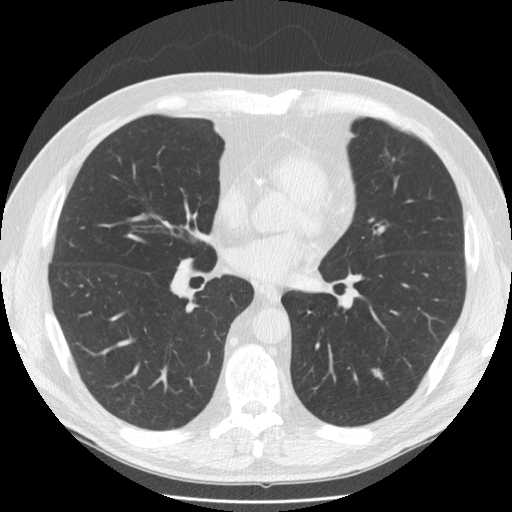
Axial slice from a low-dose chest CT screening exam, third screening round (two years after baseline), lung window (W 1500 / L -600 HU), slice 86 of 166 in the series, 512 × 512 image matrix, field of view 360 × 360 mm. Male participant, aged 58 years at enrolment. Former smoker at enrolment.
Expert reader's lesion annotation, bounding box <354,358,395,392> (left, top, right, bottom; pixels). Reader record for this screening exam (exam-level; its link to the box is not recorded): non-calcified nodule or mass ≥4 mm, left lower lobe, 10 × 7 mm, smooth margins, soft tissue attenuation, pre-existing on the prior screen: yes; interval growth: yes. Official screen result: positive, other. Participant outcome: lung cancer diagnosed 49 days after this screen — adenocarcinoma, NOS, left lower lobe, poorly differentiated (G3), stage IA (AJCC 6th edition), 8 mm at pathology.